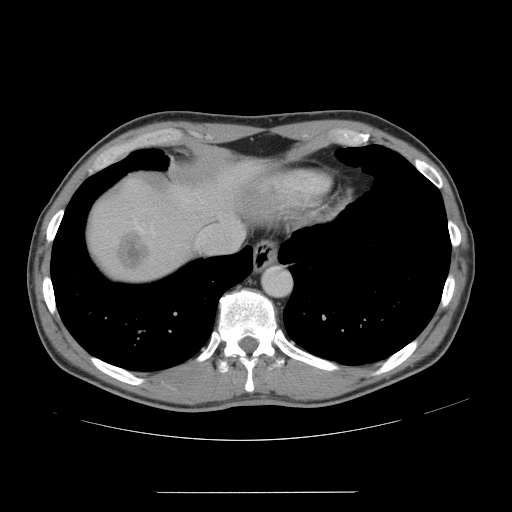
Contrast-enhanced abdominal CT, one axial slice. Slice 136 of 178 in the series (ordered by position). 120 kVp. Intravenous contrast given. Soft-tissue window (W 400 / L 40 HU). 2.5 mm slice thickness. 512 × 512 image matrix, field of view 401 × 401 mm. Male patient, age 53 years. Case-level facts recorded for this patient, not image findings: diagnosis: colorectal cancer liver metastases, imaged before liver resection; multiple liver metastases: yes; largest metastasis: 2.4 cm; disease in both lobes: no.
Annotated regions visible in this slice (expert manual segmentation):
- hepatic veins: bounding box (x1, y1, x2, y2) in pixels: (231, 231, 243, 236)
- liver: (88, 162, 260, 279)
- planned liver remnant (the part of the liver to remain after resection): (186, 162, 258, 217)
- liver metastasis: (115, 232, 147, 267)